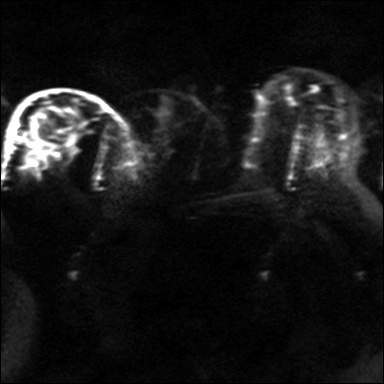
Breast MRI, one axial slice. Position 21 of 36 along the scan axis. Diffusion-weighted series; image 2 of 4 stored at this slice position (different b-values; order by instance number). 3 T. 384 × 384 image matrix, field of view 320 × 320 mm. Female patient.
Annotated regions visible in this slice (outlined manually by an expert reader):
- tumour on diffusion-weighted imaging: bounding box (x1, y1, x2, y2) in pixels: (64, 132, 79, 153)